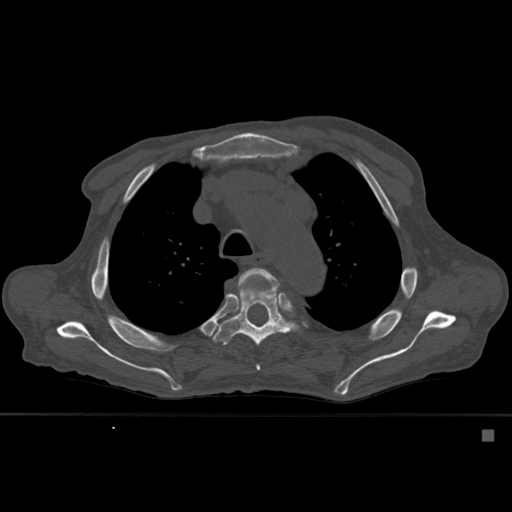
CT including the spine, one axial slice. Slice 405 of 527 in the series (ordered by position). Bone window (W 1800 / L 400 HU). 512 × 512 image matrix, field of view 373 × 373 mm. Male patient, age 78 years. From the clinical record (not read from this slice): primary cancer: prostate.
Outlined on this slice (semi-automatic segmentation, software-assisted and operator-edited):
- T4 vertebra: box from (x=236, y=268) to (x=278, y=371) px
- T5 vertebra: (x=213, y=268)–(x=296, y=347)